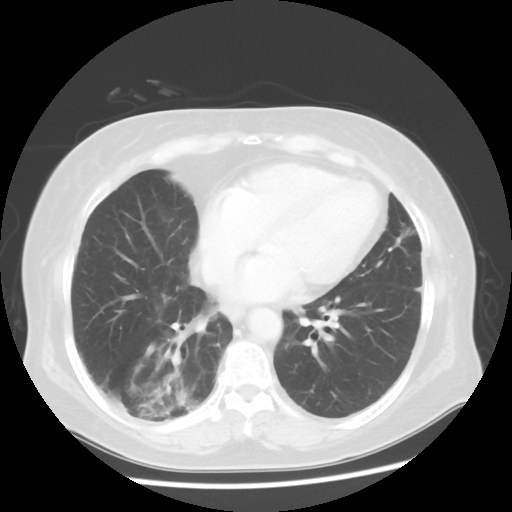
Chest CT, one axial slice. Slice 21 of 56 in the series (ordered by position). 120 kVp. Lung window (W 1500 / L -600 HU). 5 mm slice thickness. 512 × 512 image matrix. Female patient, age 64 years. From the clinical record (not read from this slice): clinical TNM (as recorded): Tis N0 M0.
Outlined on this slice (bounding box drawn by a radiologist):
- lung tumour (recorded histology: adenocarcinoma): bounding box (x1, y1, x2, y2) in pixels: (124, 365, 196, 439)